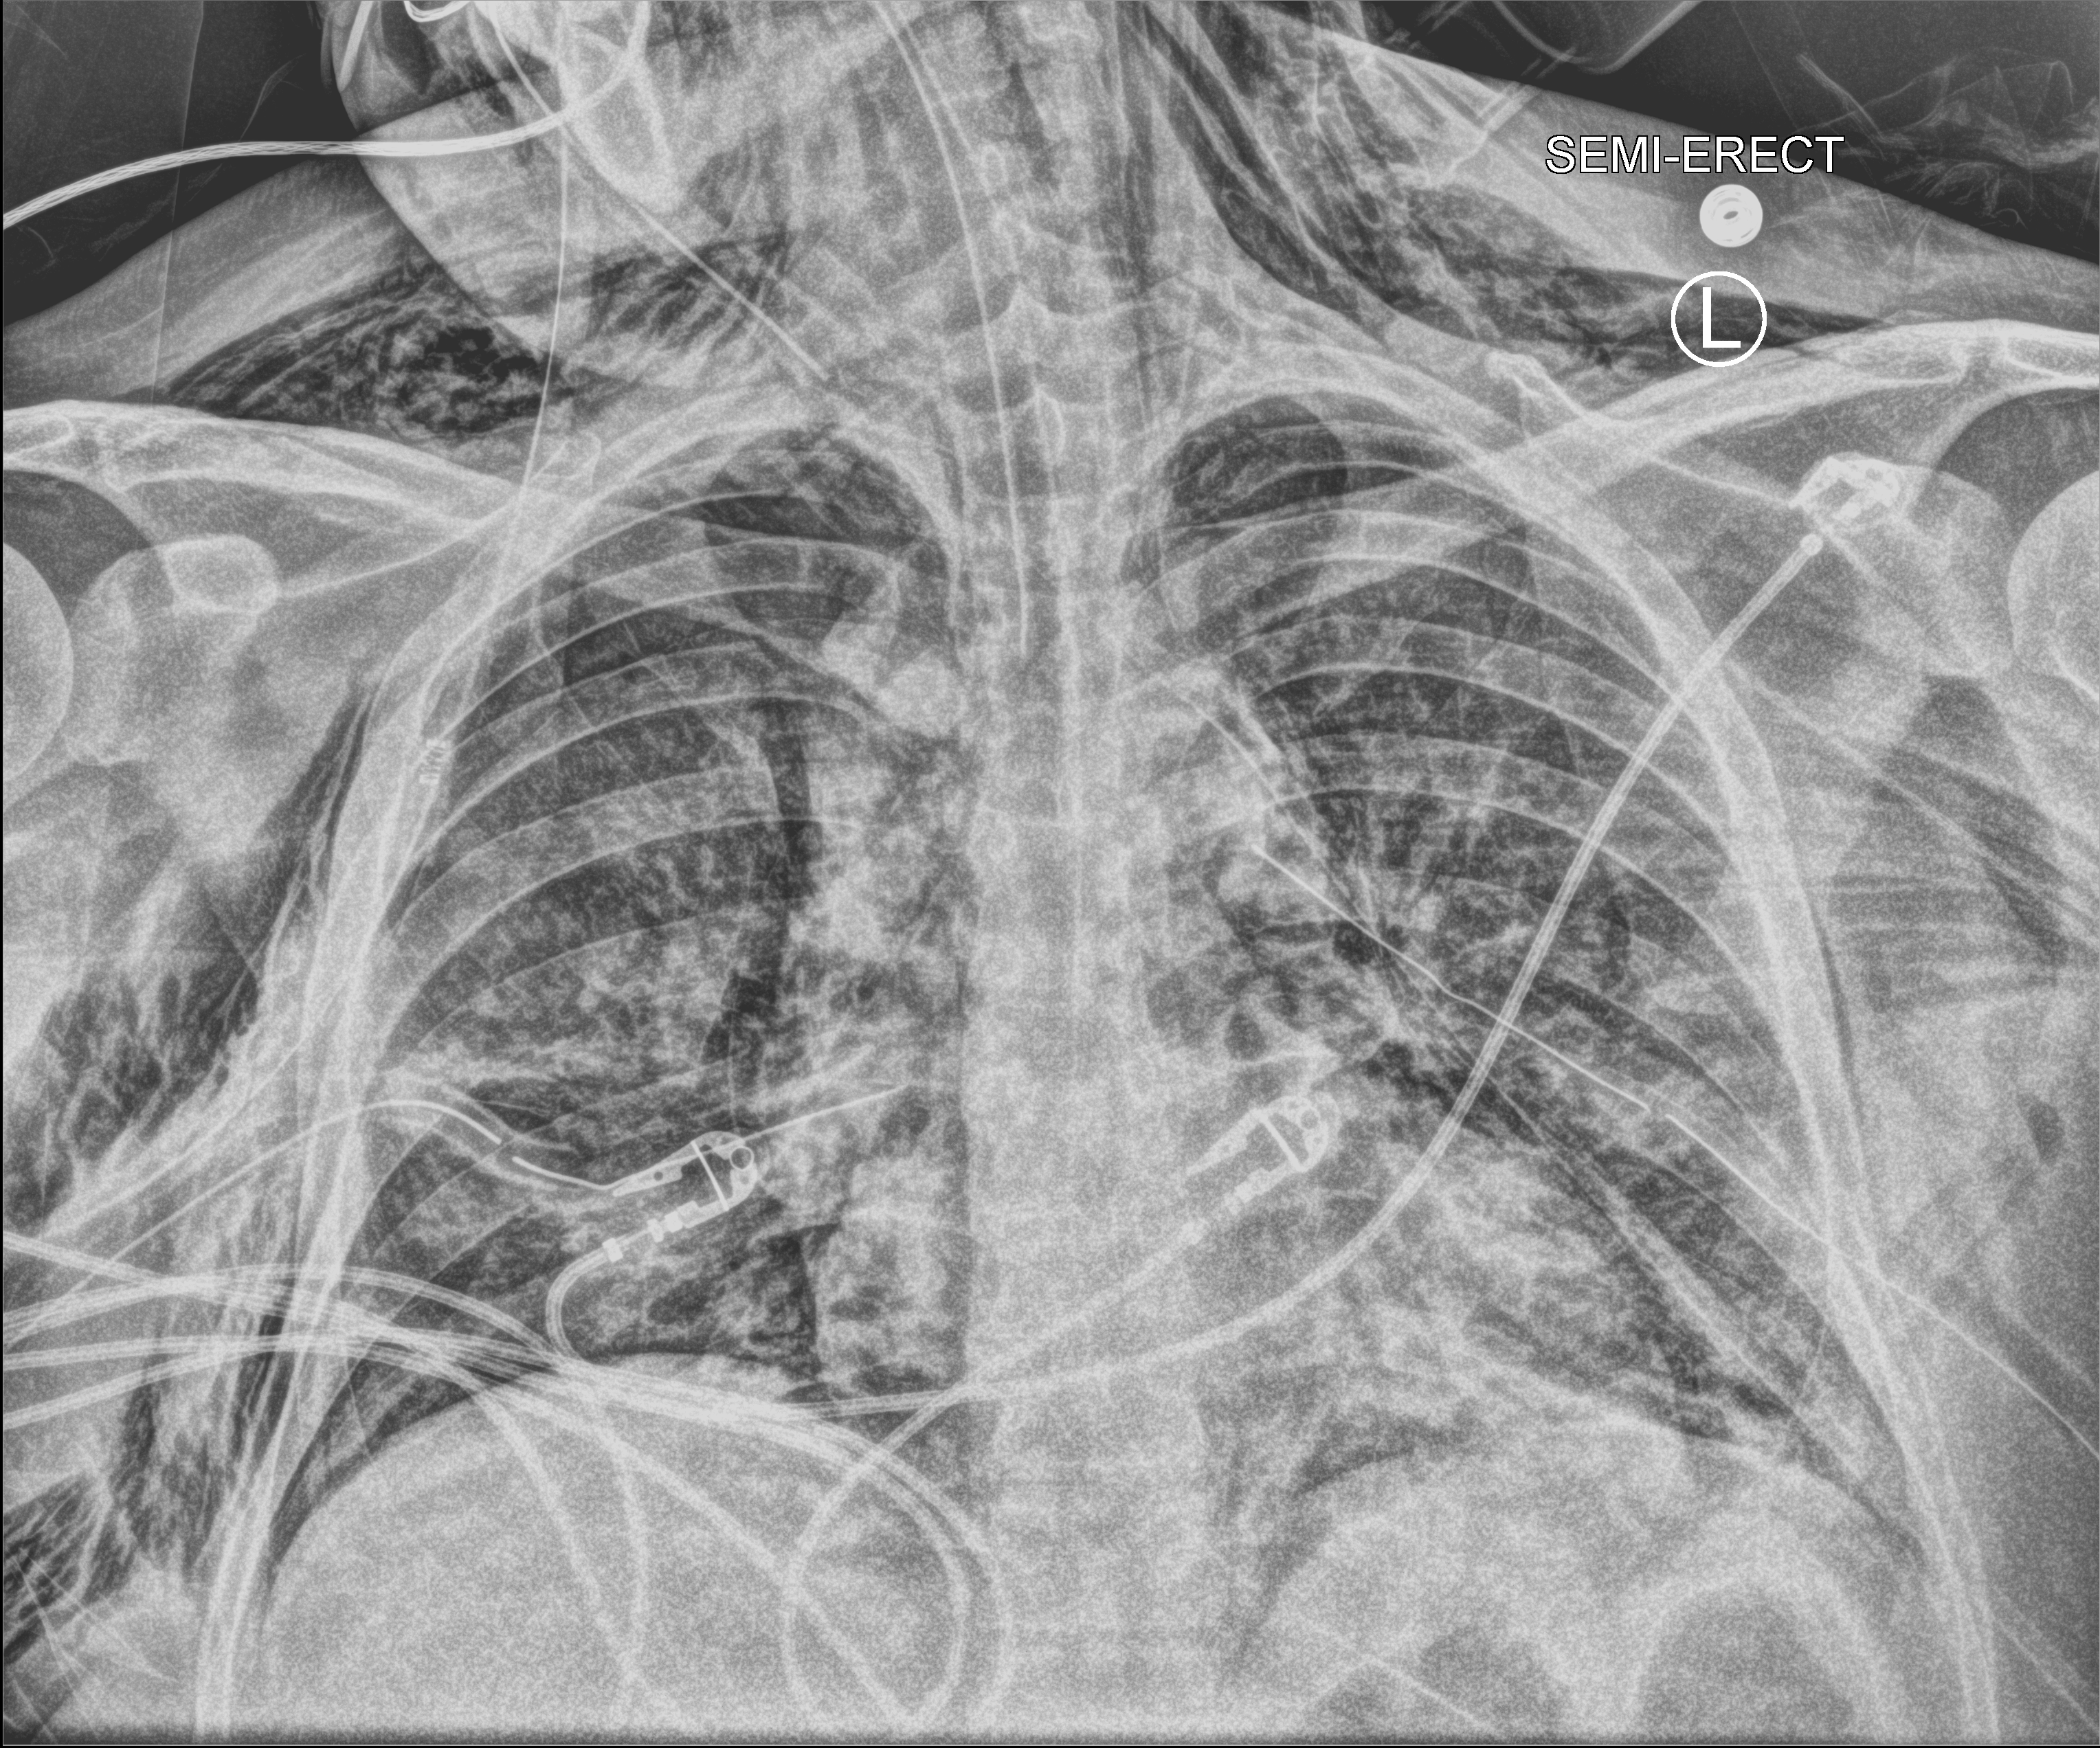
Bedside chest radiograph (computed radiography). Male patient hospitalised with COVID-19, age 18–59 years.
Admission-level facts for this patient (not findings on this image; timing relative to this image not recorded):
- admitted to intensive care during this hospital stay: yes
- diabetes (admission record): yes